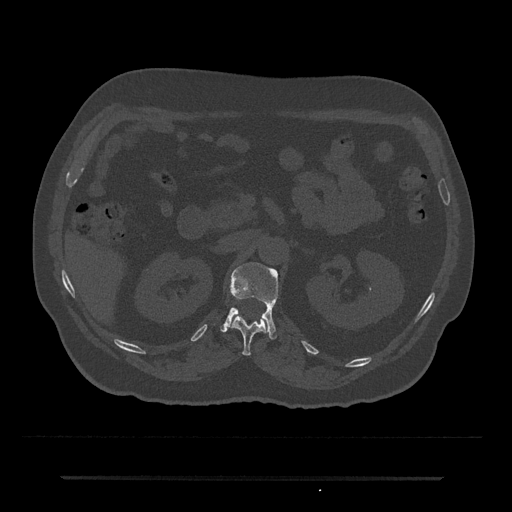
CT including the spine, one axial slice. Position 99 of 797 along the scan axis. 120 kVp. Bone window (W 1800 / L 400 HU). 0.5 mm slice thickness. 512 × 512 image matrix, field of view 437 × 437 mm. Male patient, age 69 years. From the clinical record (not read from this slice): primary cancer: prostate.
Structures marked on this image (semi-automatically segmented with operator editing):
- L1 vertebra: bounding box (x1, y1, x2, y2) in pixels: (221, 262, 279, 339)
- T12 vertebra: (231, 313, 269, 355)